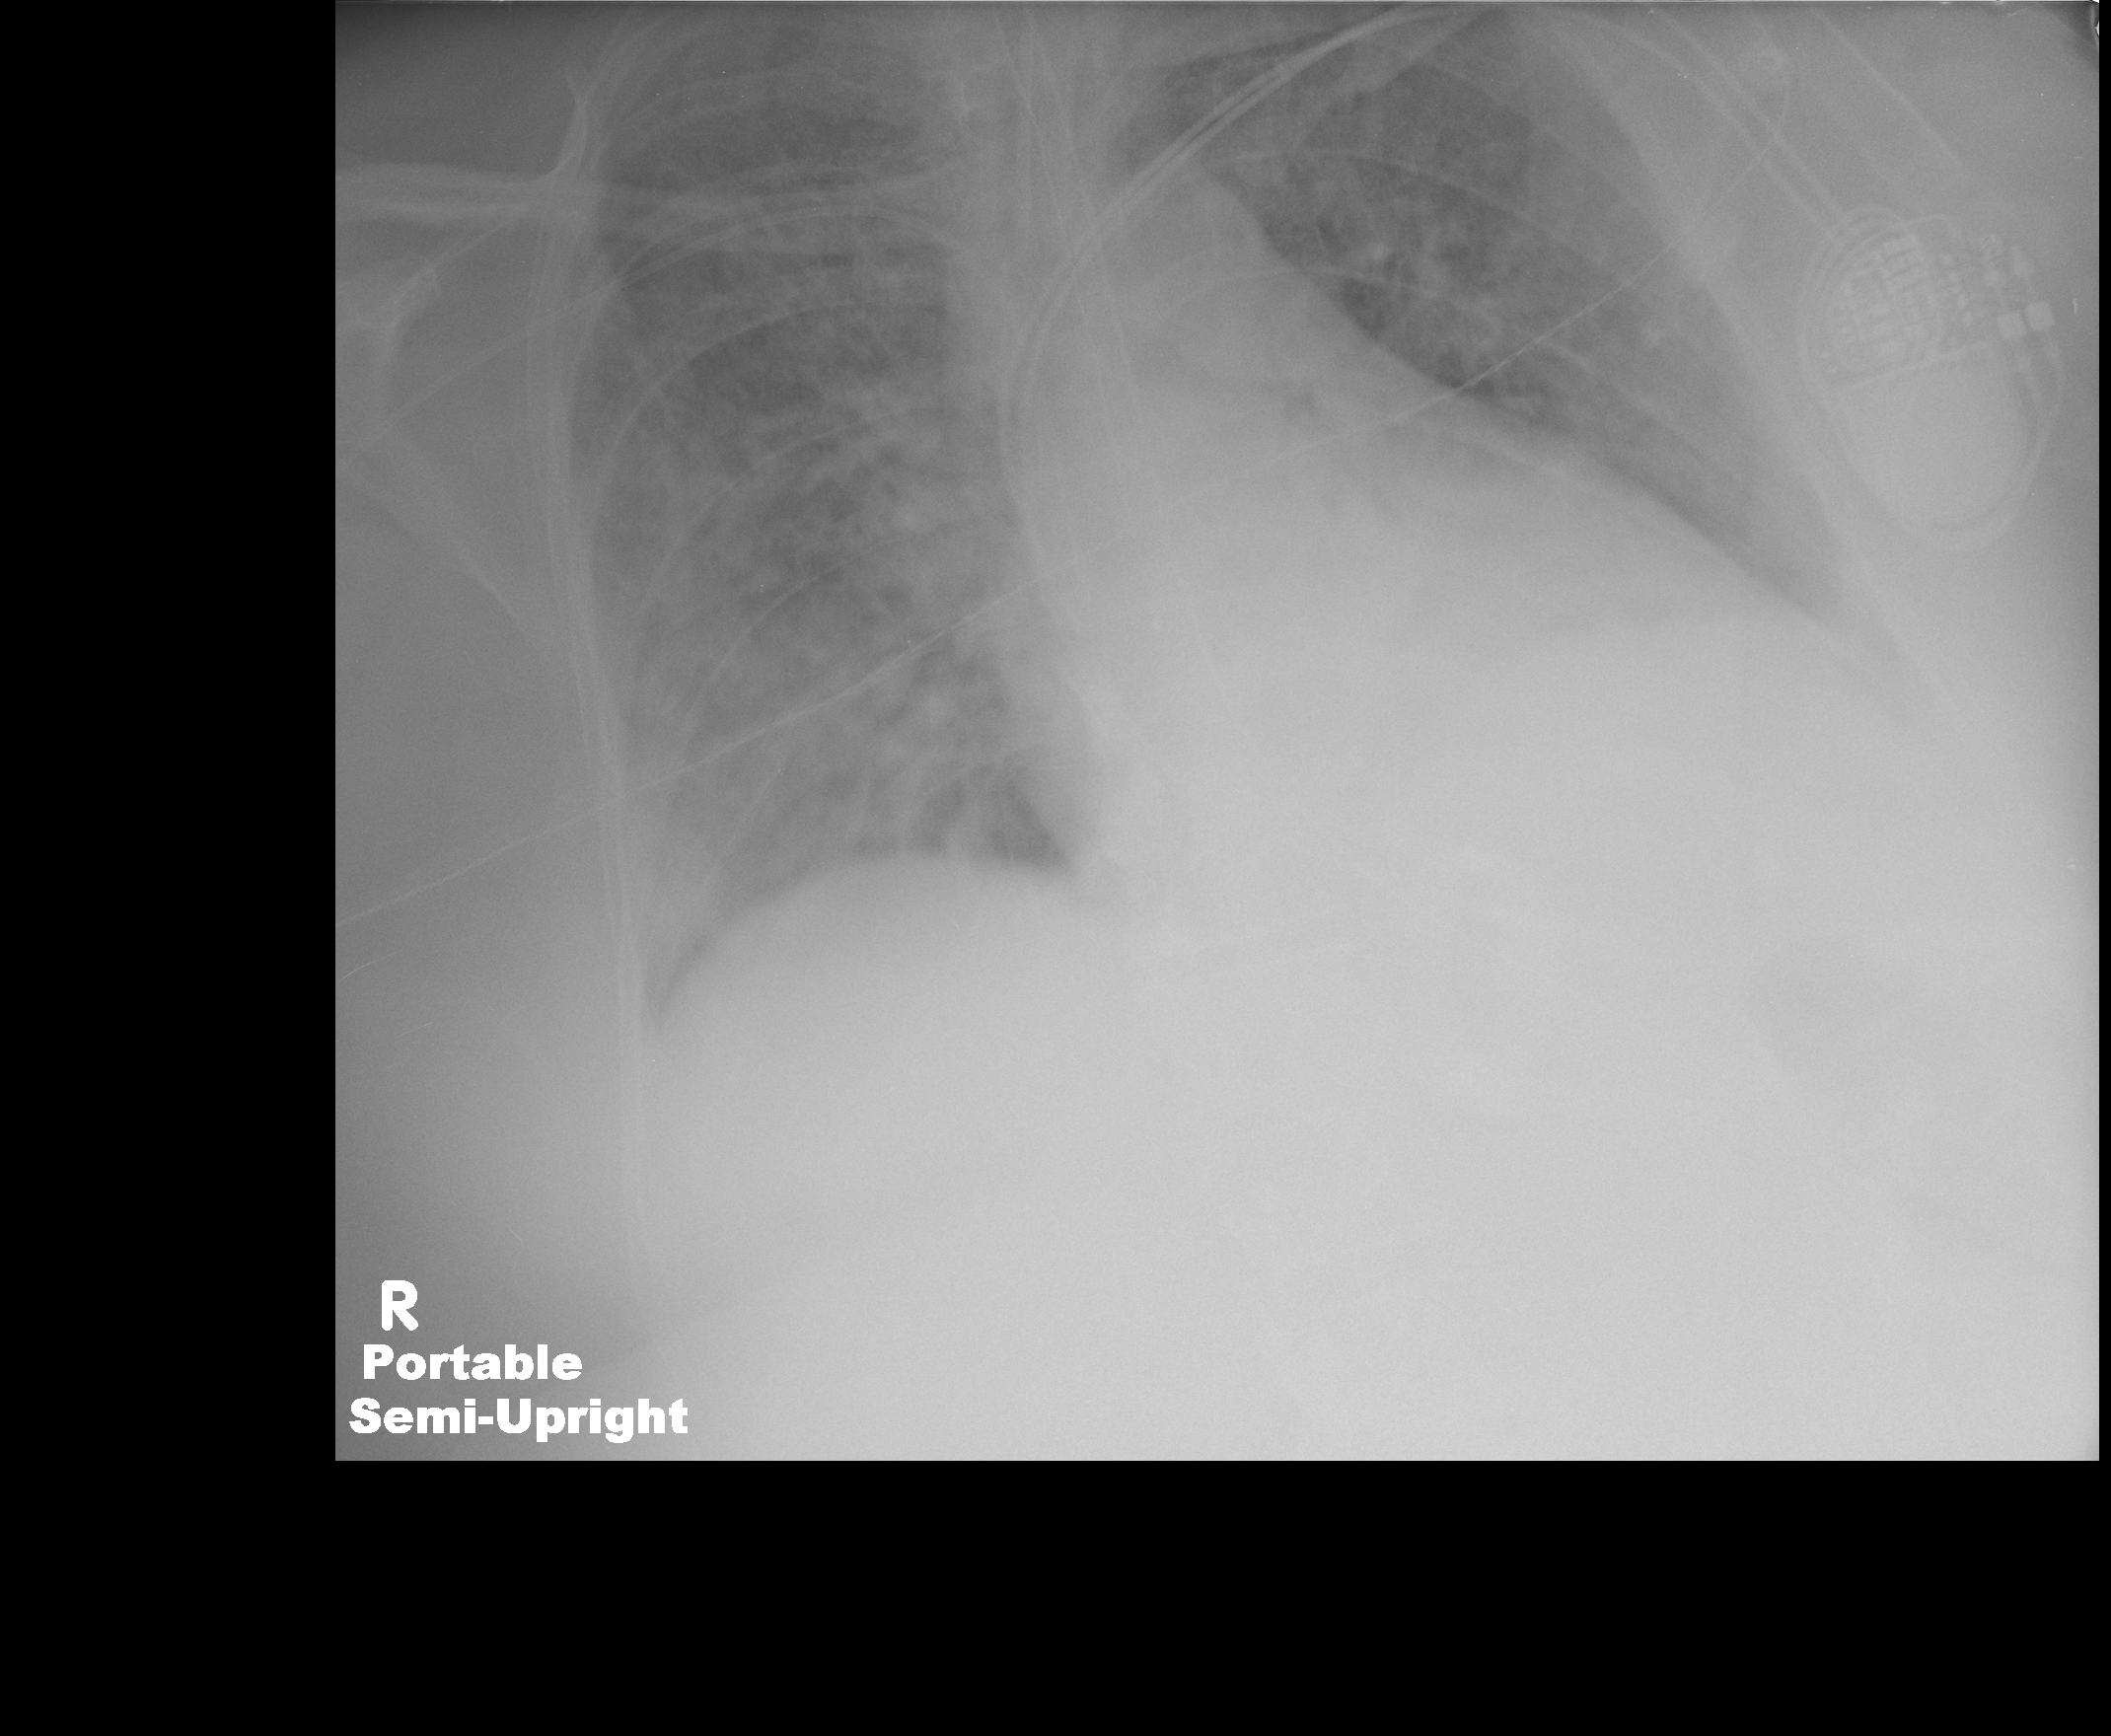
Portable chest radiograph, AP projection. Female patient, age 57 years; imaged 7 days after the COVID-19 diagnosis.
Radiologist key findings (as recorded): Persistent perhaps somewhat more diffuse bilateral airspace disease.